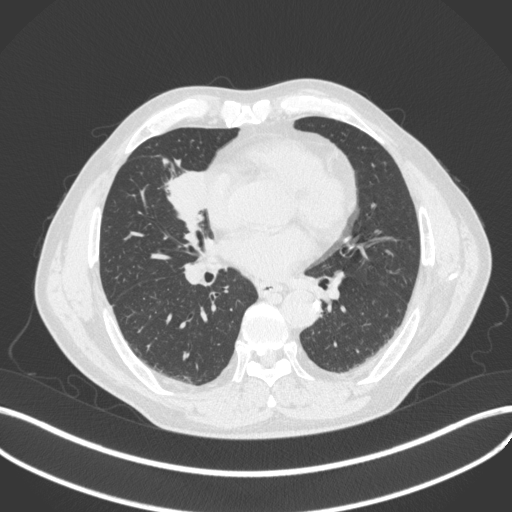
Chest CT, one axial slice. Slice 188 of 429 in the series (ordered by position). Reconstruction kernel B31f. Lung window (W 1500 / L -600 HU). 512 × 512 image matrix, field of view 400 × 400 mm. Male patient, age 61 years. From the clinical record (not read from this slice): clinical TNM (as recorded): T2b N1 M0.
Annotated regions visible in this slice (bounding box drawn by a radiologist):
- lung tumour (recorded histology: squamous cell carcinoma): bounding box (x1, y1, x2, y2) in pixels: (158, 157, 218, 233)